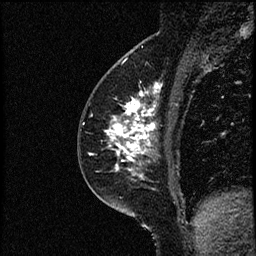
Breast MRI (dynamic contrast-enhanced), one sagittal slice. Slice 31 of 52 in the series (ordered by position). Dynamic contrast-enhanced study with each time point stored as its own series, time point 2 of 3 at this slice position (early post-contrast, ordered by acquisition time). 1.5 T. TE 4.2 ms, TR 17.6 ms. 2 mm slice thickness. 256 × 256 image matrix, field of view 200 × 200 mm. Patient: female, 49 years. Case-level facts recorded for this patient, not image findings: setting: breast cancer imaged before/during neoadjuvant chemotherapy; receptor status: HER2-positive.
Outlined on this slice (semi-automatically segmented with operator editing):
- analysis volume of interest (the breast-tissue region the enhancement analysis was run in; not a lesion): bounding box (x1, y1, x2, y2) in pixels: (85, 65, 182, 175)
- tumour enhancement mask (voxels above the 100 % enhancement threshold inside the analysis volume of interest): (105, 87, 159, 175)